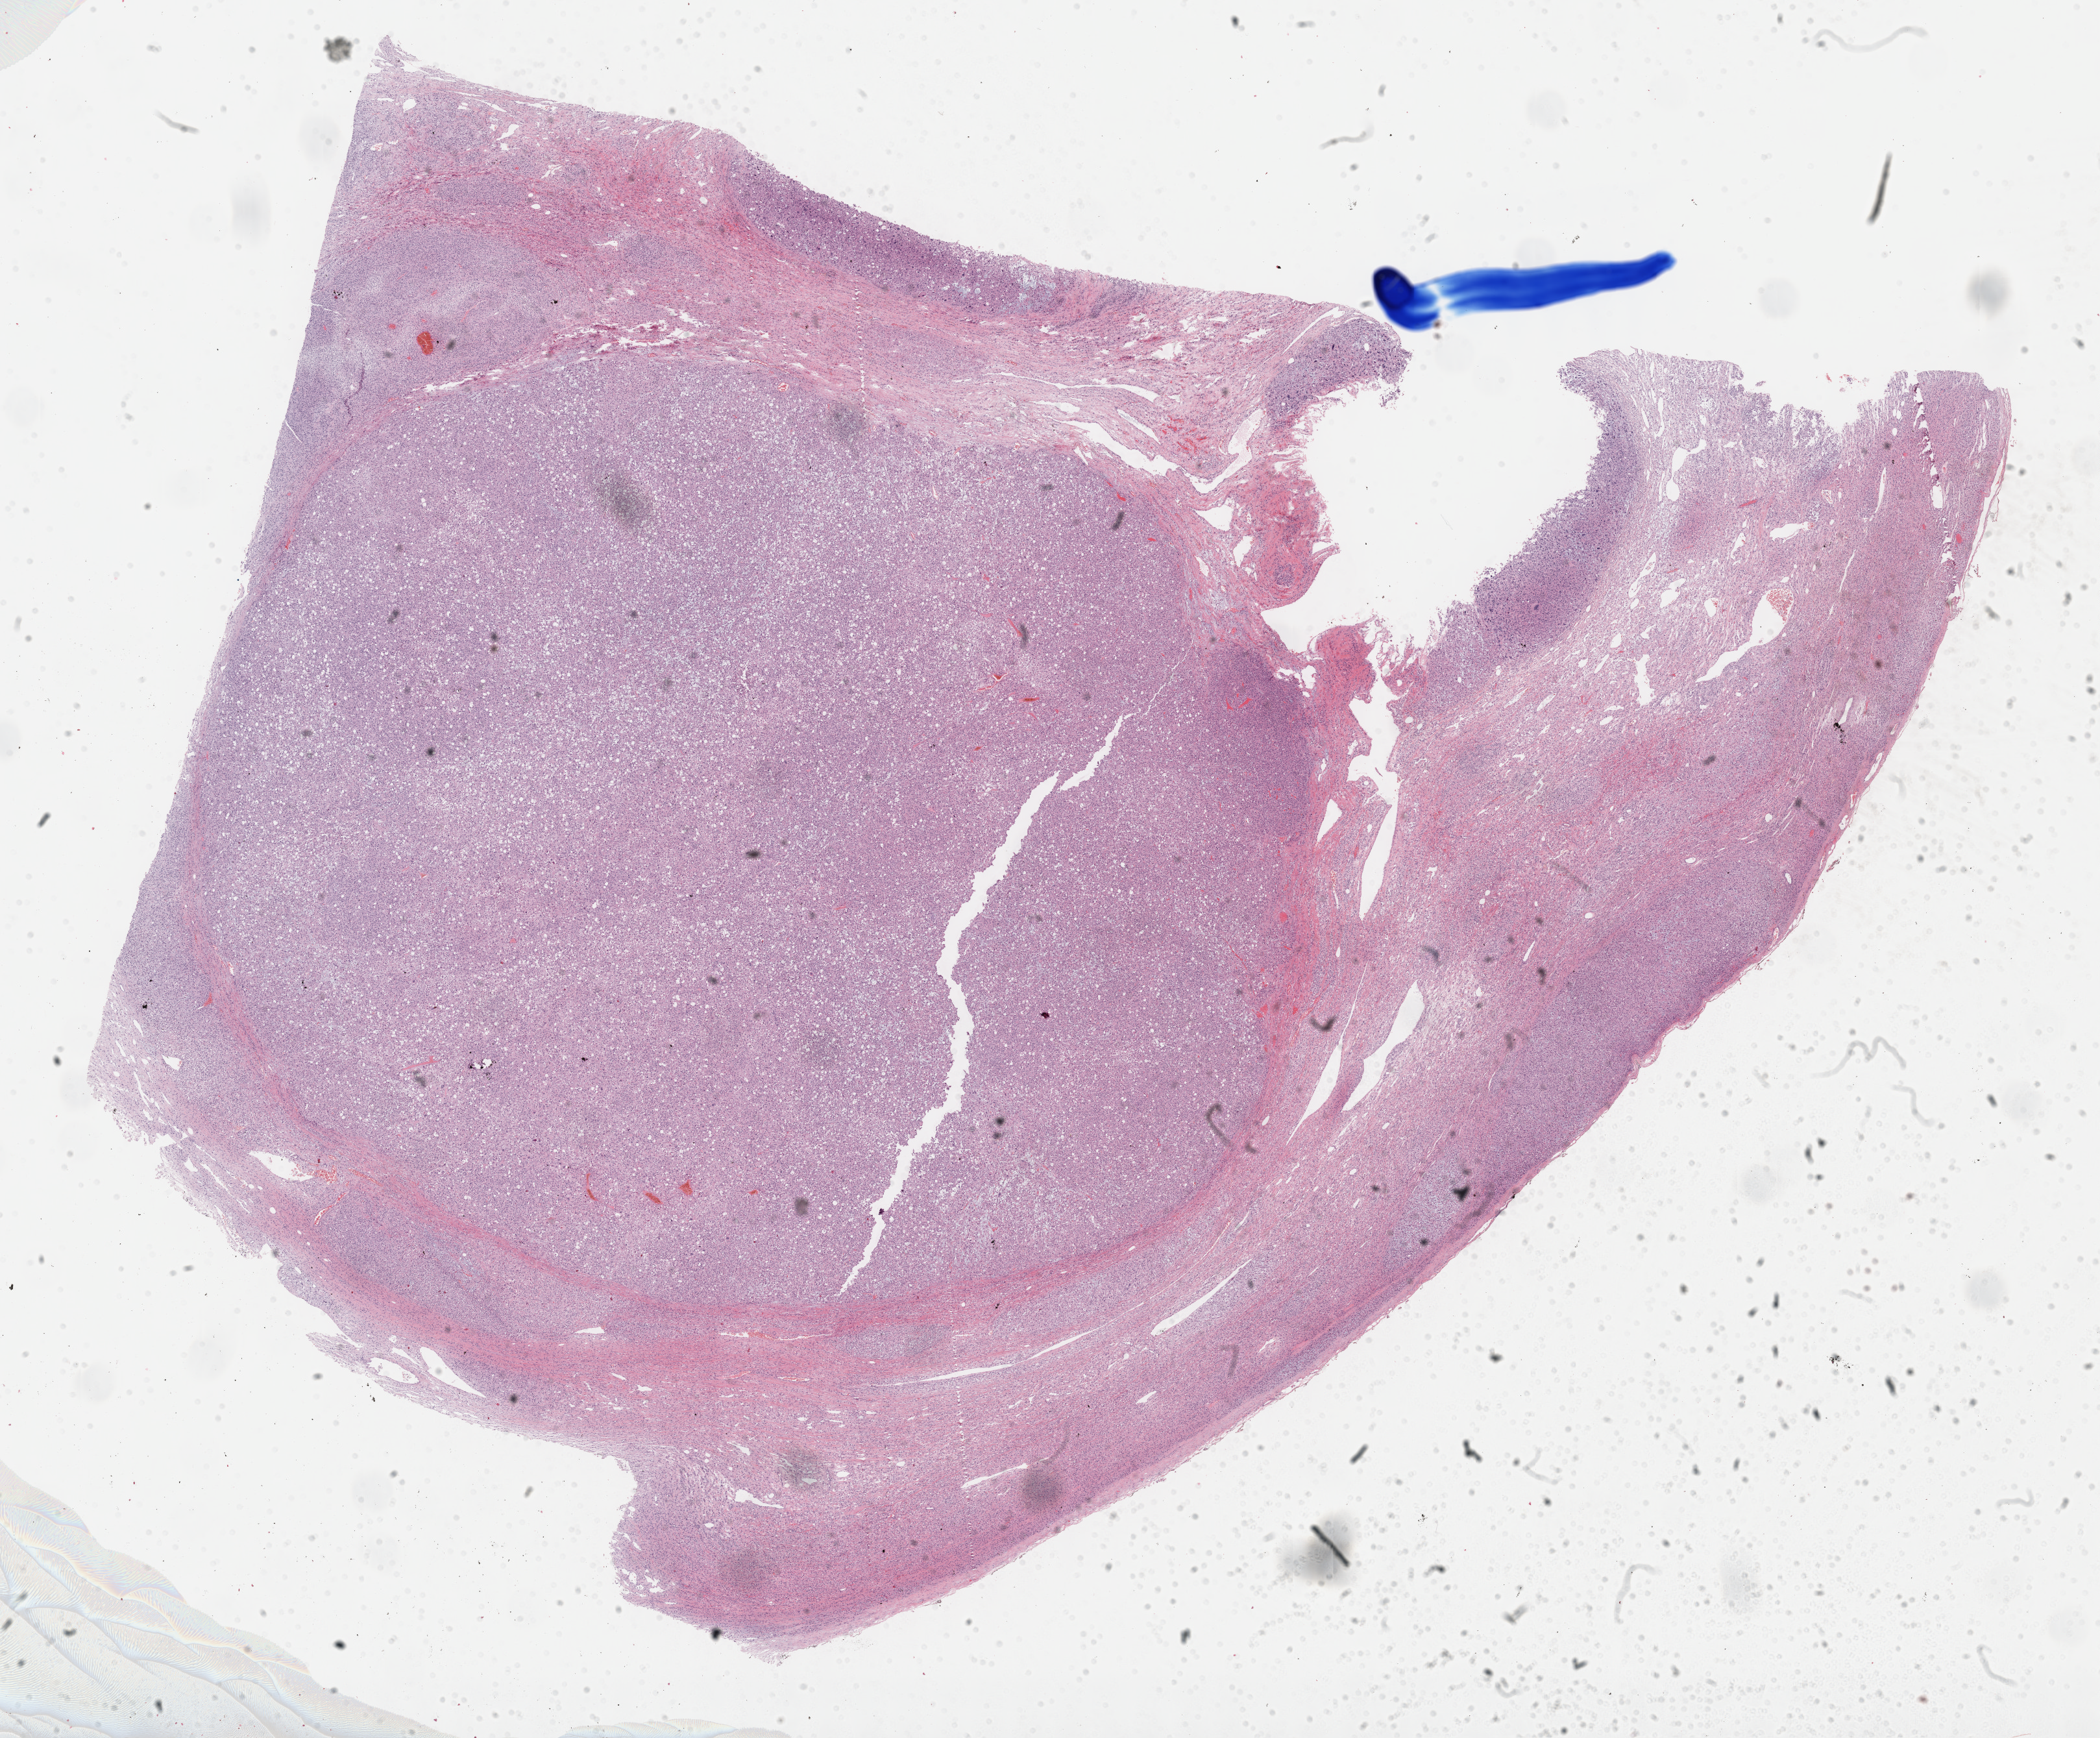
Whole-slide histology image, Hematoxylin and eosin (H&E) stained, a low-resolution overview of the entire scanned area, about 26.2 x 21.7 mm (acquisition: 40x scan); formalin-fixed paraffin-embedded (FFPE) diagnostic section; sample: primary tumour, adrenal cortex. Patient: male, age at initial diagnosis 40 years.
Diagnosis: Adrenal cortical carcinoma (cortex of adrenal gland).